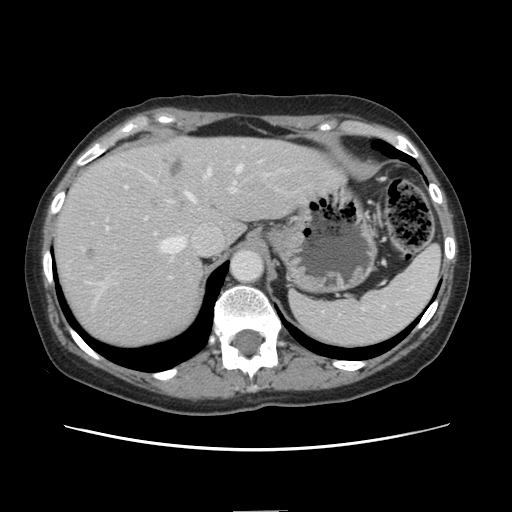
Contrast-enhanced abdominal CT, one axial slice. Position 109 of 141 along the scan axis. 120 kVp. Intravenous contrast given. Soft-tissue window (W 400 / L 40 HU). 2.5 mm slice thickness. 512 × 512 image matrix. Female patient, age 63 years. Case-level facts recorded for this patient, not image findings: diagnosis: colorectal cancer liver metastases, imaged before liver resection; multiple liver metastases: yes; largest metastasis: 3.2 cm; disease in both lobes: yes.
Annotated regions visible in this slice (outlined manually by an expert reader):
- hepatic veins: bounding box <96,166,242,300> (left, top, right, bottom; pixels)
- liver: <54,138,340,349>
- planned liver remnant (the part of the liver to remain after resection): <190,138,341,242>
- portal vein (with intrahepatic branches): <205,172,236,193>